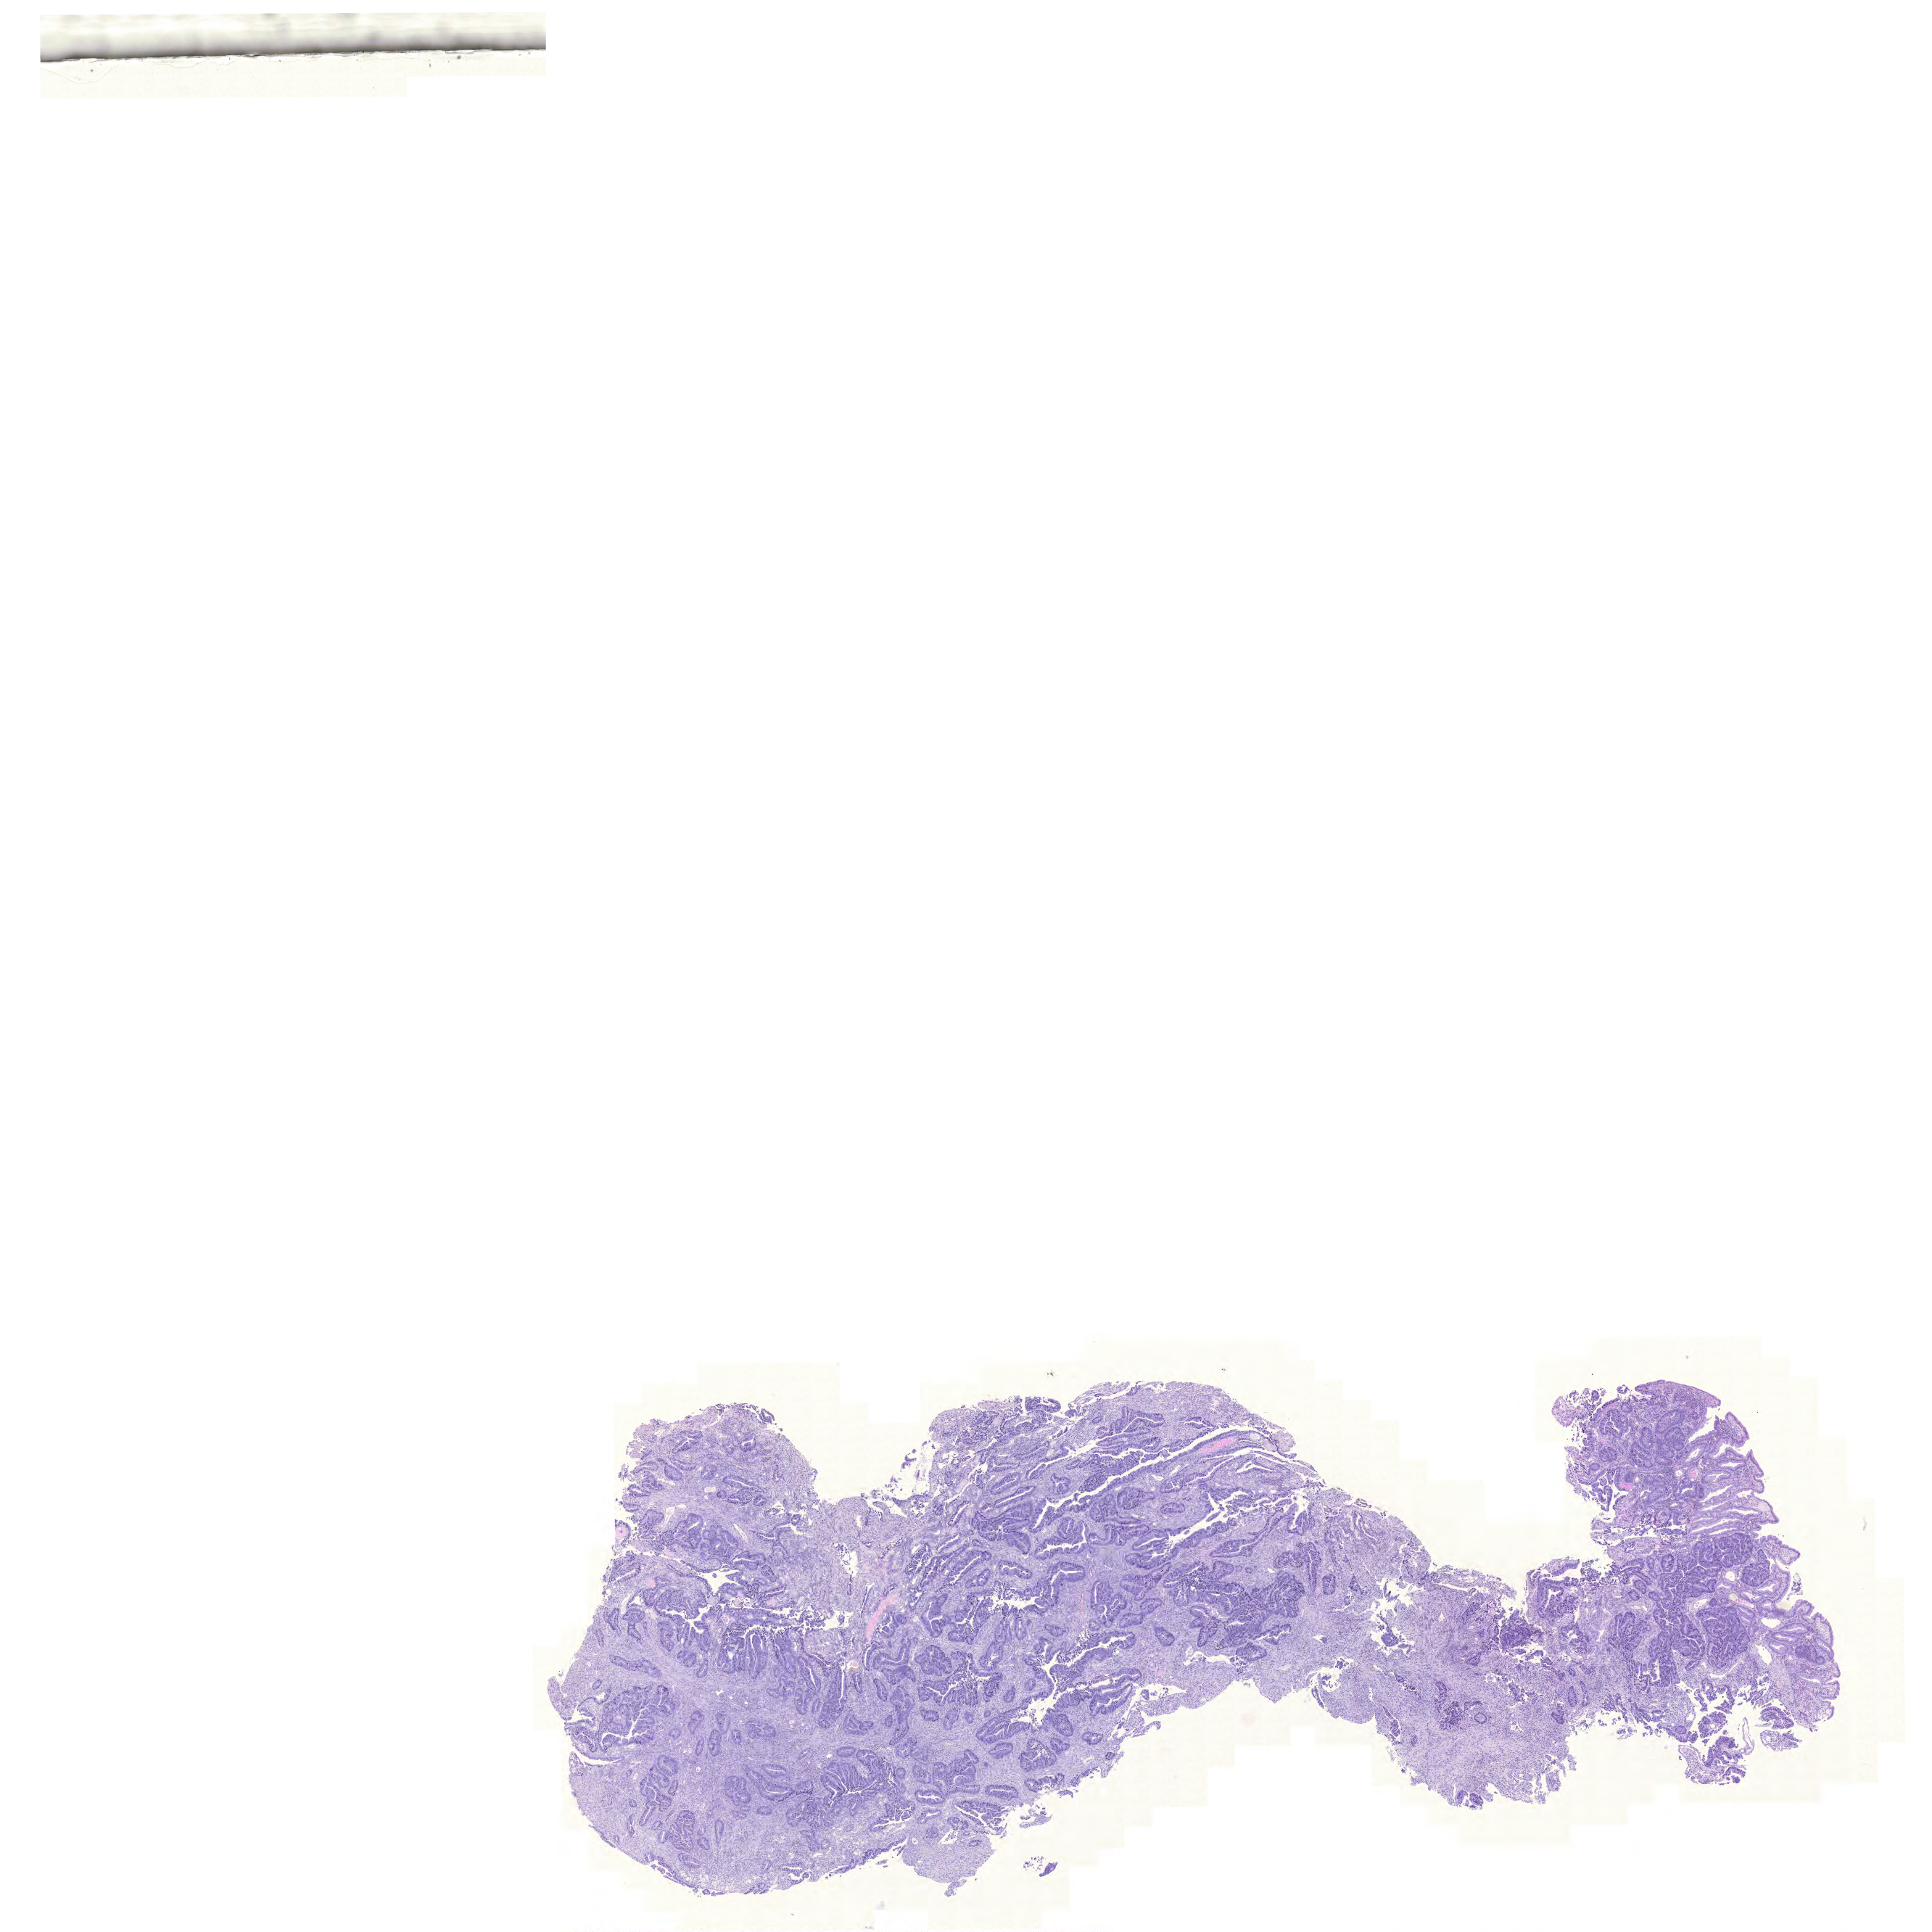
Digitized H&E-stained tissue section (whole slide) — low-resolution overview of the scanned area, about 19.8 x 19.8 mm (from a 20x scan), FFPE section, rectum, primary tumour sample. Female patient; age at initial diagnosis 74 years.
Histologic diagnosis: Adenocarcinoma, NOS (rectosigmoid junction).